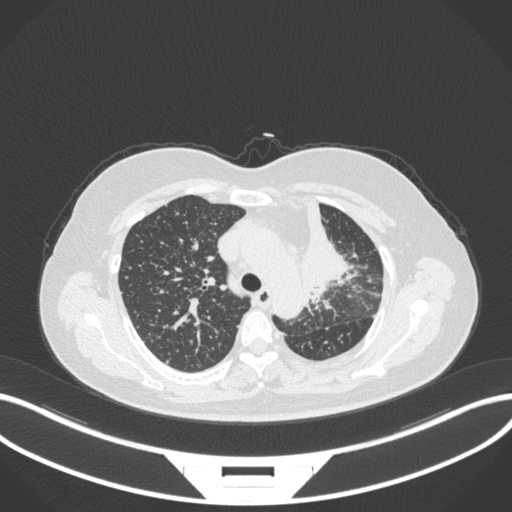
Chest CT, one axial slice. Slice 242 of 348 in the series (ordered by position). Reconstruction kernel B31f. Lung window (W 1500 / L -600 HU). 512 × 512 image matrix, field of view 400 × 400 mm. Female patient, age 49 years. Case-level facts recorded for this patient, not image findings: clinical TNM (as recorded): T1c N0 M1.
Structures marked on this image (rectangle marked by the reading radiologist):
- lung tumour (recorded histology: adenocarcinoma): bounding box (x1, y1, x2, y2) in pixels: (298, 196, 355, 303)